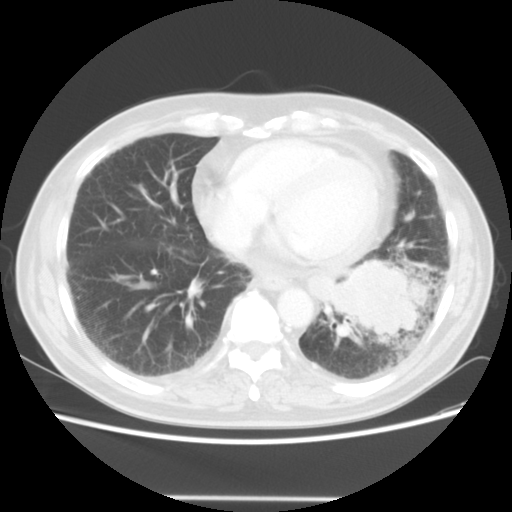
Chest CT, one axial slice; reconstruction kernel STANDARD; 140 kVp; lung window (W 1500 / L -600 HU); 5 mm slice thickness; 512 × 512 image matrix, field of view 360 × 360 mm. Patient: male, 66 years. From the clinical record (not read from this slice): clinical TNM (as recorded): T4 N3 M0; histopathological grade: G3.
Annotated regions visible in this slice (rectangle marked by the reading radiologist):
- lung tumour (recorded histology: small cell carcinoma): box from (x=339, y=256) to (x=437, y=338) px